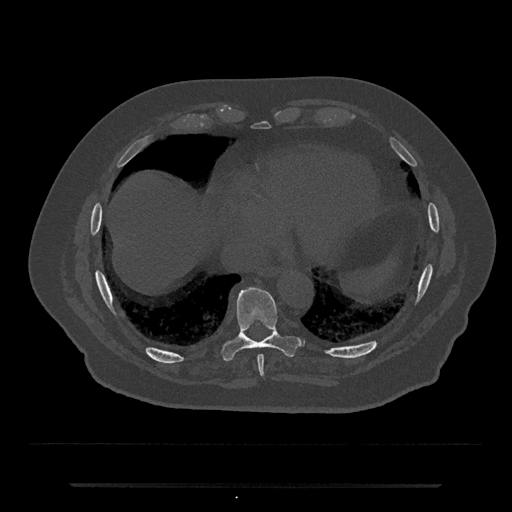
CT including the spine, one axial slice. Slice 763 of 797 in the series (ordered by position). Bone window (W 1800 / L 400 HU). 0.5 mm slice thickness. 512 × 512 image matrix. Male patient, age 80 years. From the clinical record (not read from this slice): primary cancer: prostate; vertebrae with lytic lesions (as recorded): L1, T11.
Structures marked on this image (semi-automatic segmentation, software-assisted and operator-edited):
- T8 vertebra: box from (x=257, y=355) to (x=264, y=377) px
- T9 vertebra: (x=222, y=285)–(x=302, y=361)